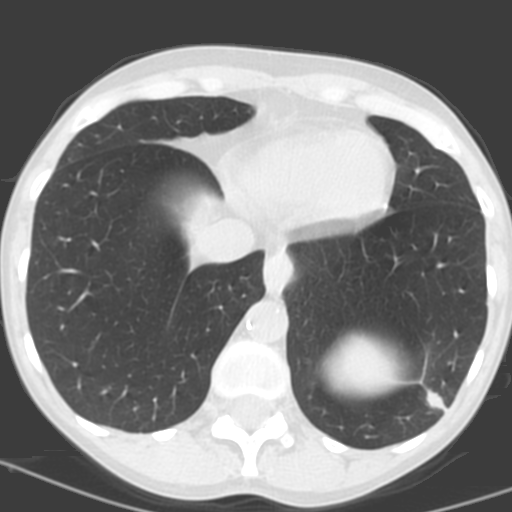
Low-dose screening chest CT, one axial slice. Position 41 of 156 along the scan axis. 120 kVp. Lung window (W 1500 / L -600 HU). 3.2 mm slice thickness. 512 × 512 image matrix, field of view 262 × 262 mm.
Structures marked on this image (expert manual segmentation):
- lesion 1 (tumor, lower lobe of left lung): bounding box <426,389,447,412> (left, top, right, bottom; pixels)